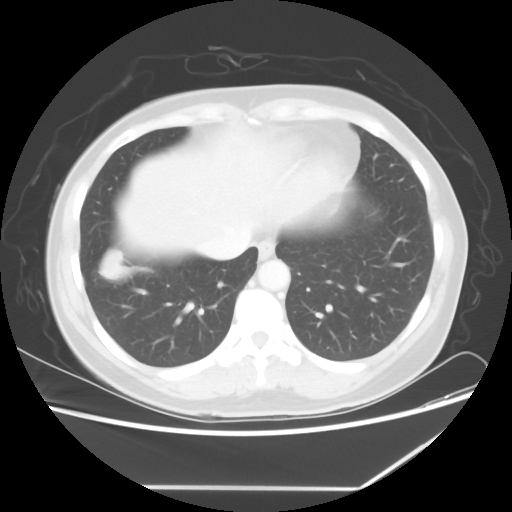
Chest CT, one axial slice. Slice 19 of 60 in the series (ordered by position). Reconstruction kernel STANDARD. Lung window (W 1500 / L -600 HU). 5 mm slice thickness. 512 × 512 image matrix, field of view 374 × 374 mm. Female patient, age 42 years. Case-level facts recorded for this patient, not image findings: clinical TNM (as recorded): T2 N1 M0.
Outlined on this slice (rectangle marked by the reading radiologist):
- lung tumour (recorded histology: adenocarcinoma): bounding box (x1, y1, x2, y2) in pixels: (98, 243, 128, 281)